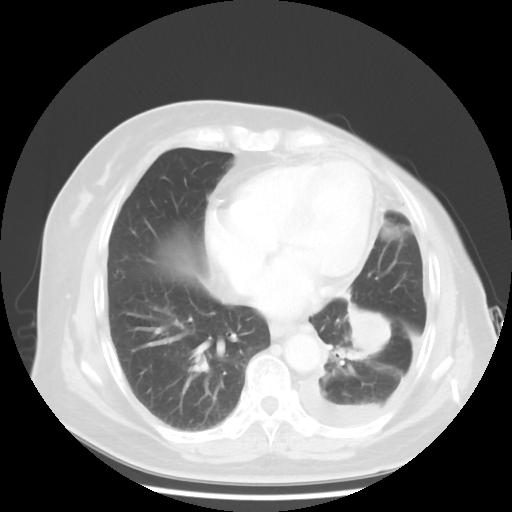
Chest CT, one axial slice. Position 16 of 48 along the scan axis. Reconstruction kernel STANDARD. 120 kVp. Lung window (W 1500 / L -600 HU). 512 × 512 image matrix, field of view 360 × 360 mm. Female patient, age 63 years. From the clinical record (not read from this slice): clinical TNM (as recorded): T2 N0 M1.
Outlined on this slice (rectangle marked by the reading radiologist):
- lung tumour (recorded histology: adenocarcinoma): bounding box [x1, y1, x2, y2] px = [339, 303, 400, 369]